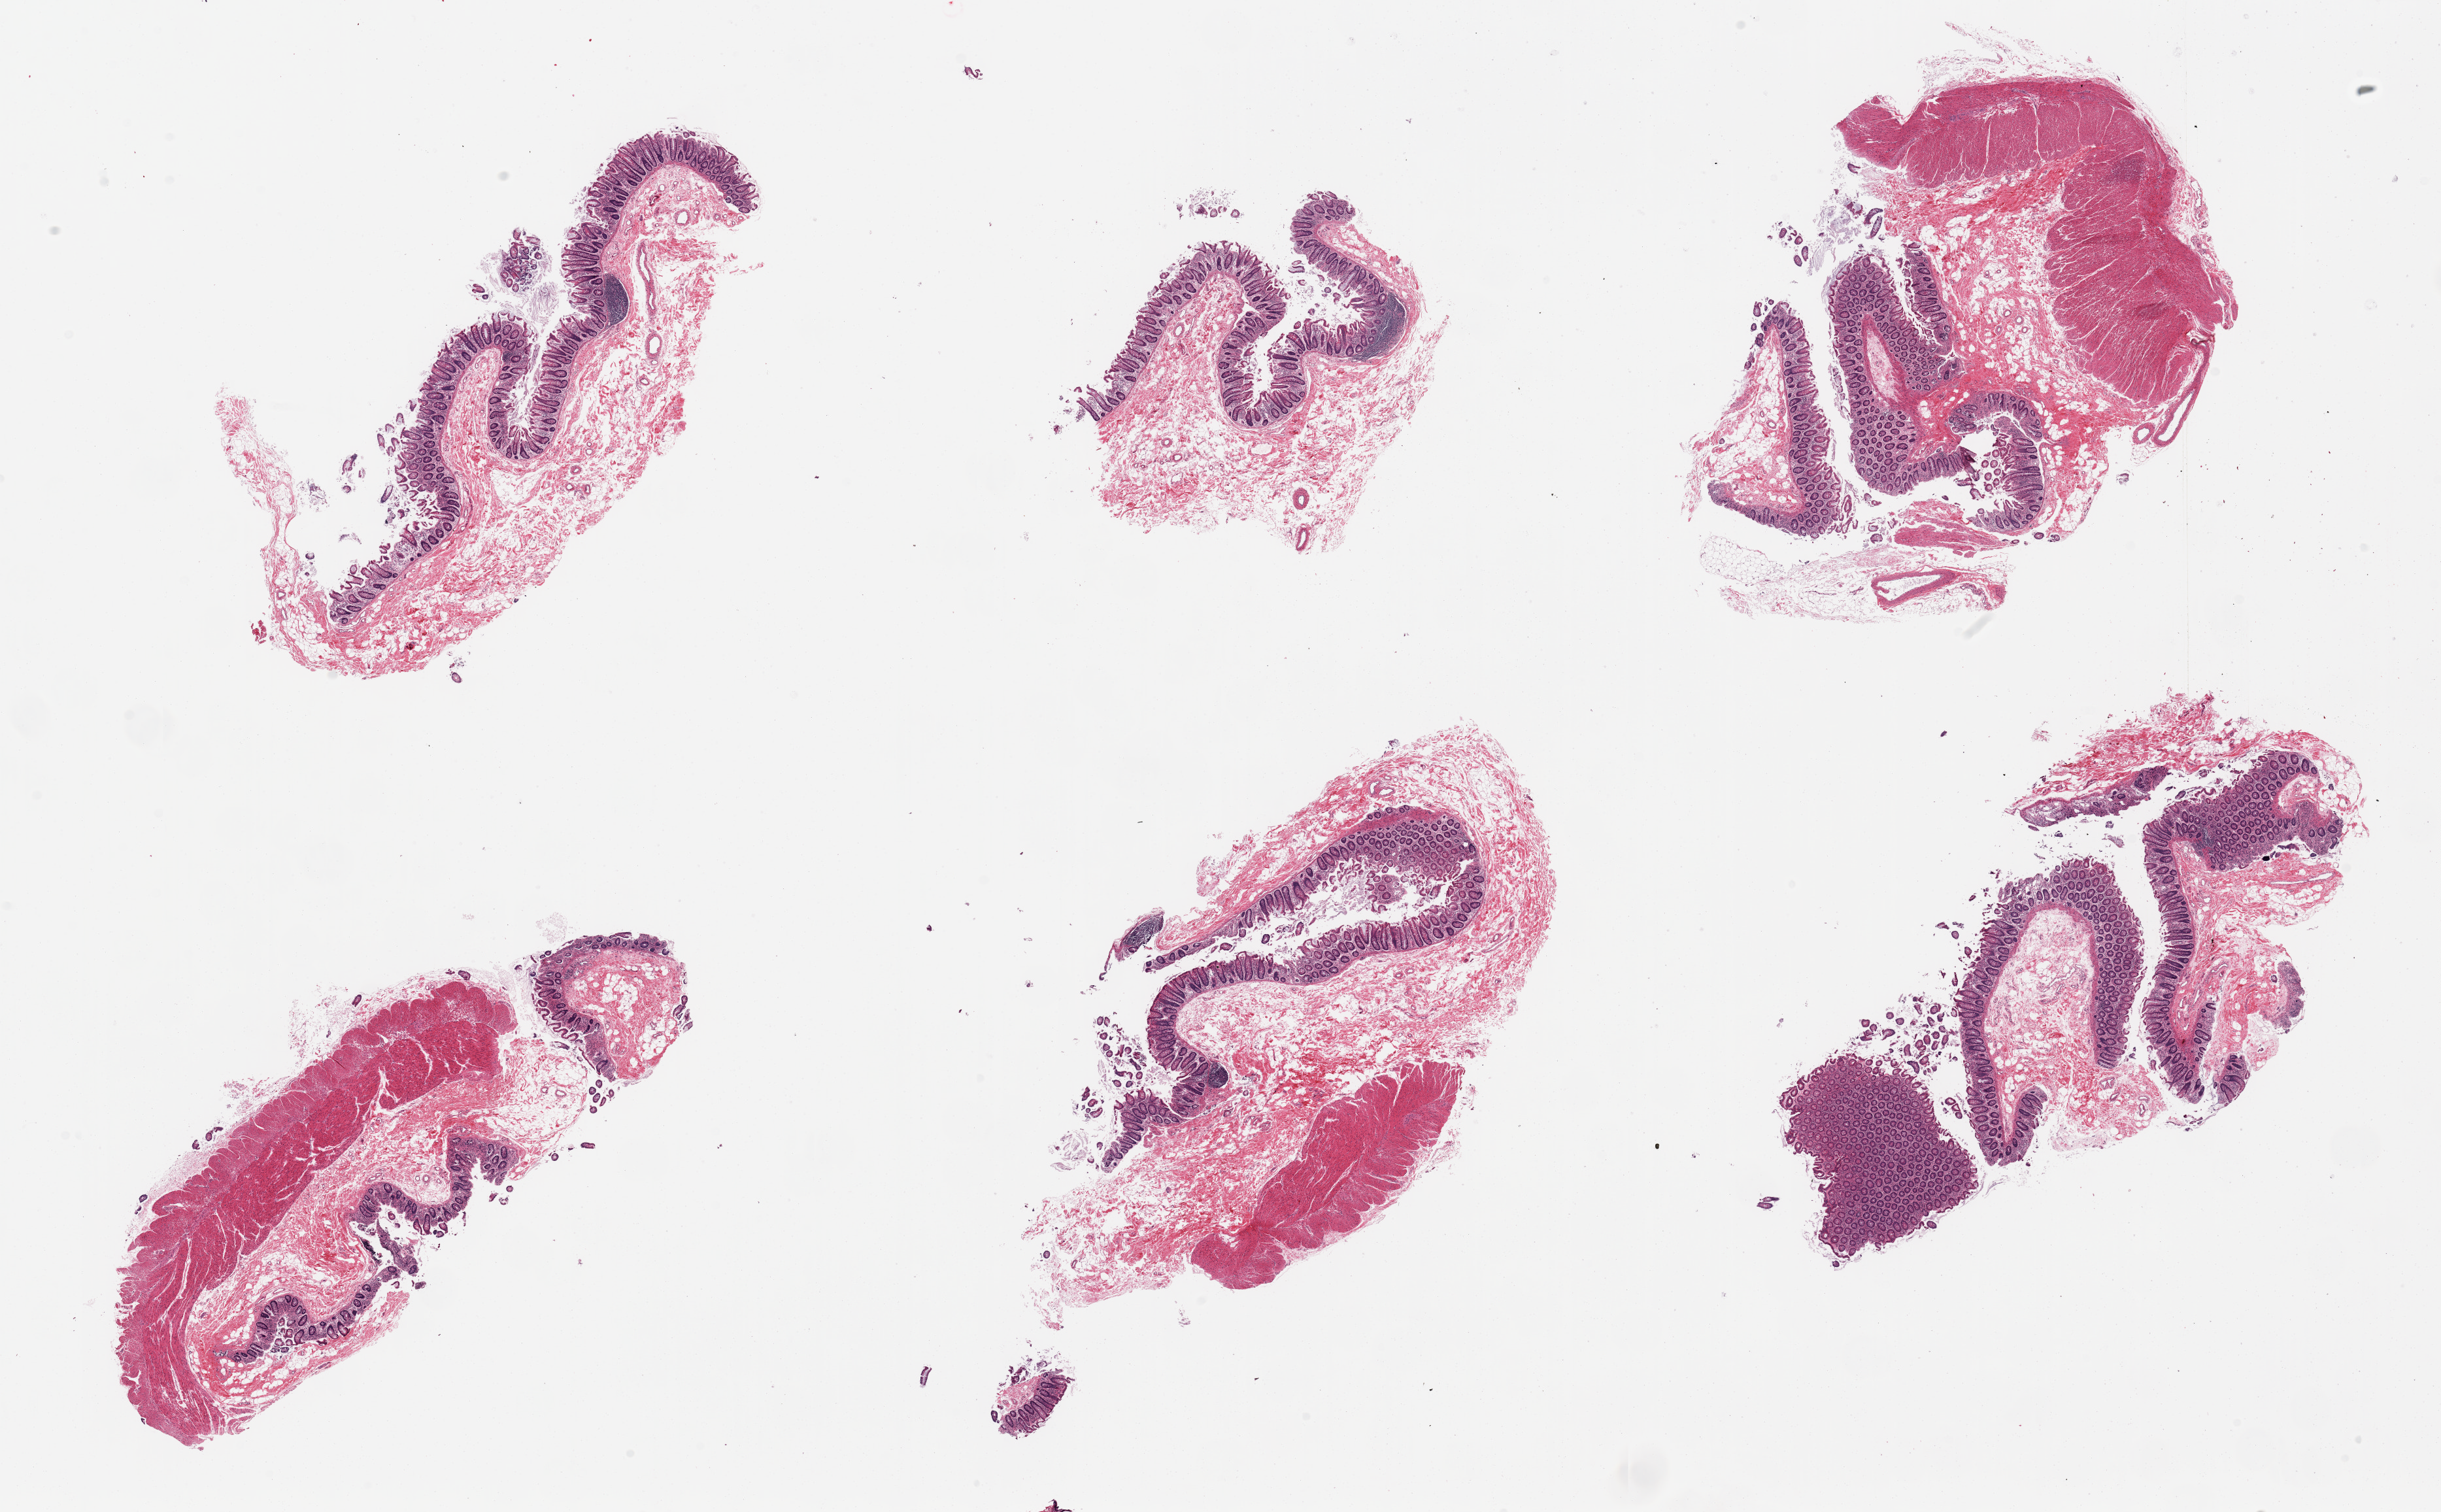
Haematoxylin and eosin whole-slide image — low-resolution overview of the scanned area, about 29.5 x 18.3 mm (from a 20x scan). PAXgene-fixed, paraffin-embedded tissue. Section of transverse colon (target tissue). Tissue donor sample. Donor: female.
* review note (as recorded): 6 pieces; 3 are mucosa only, 3 are full thickness